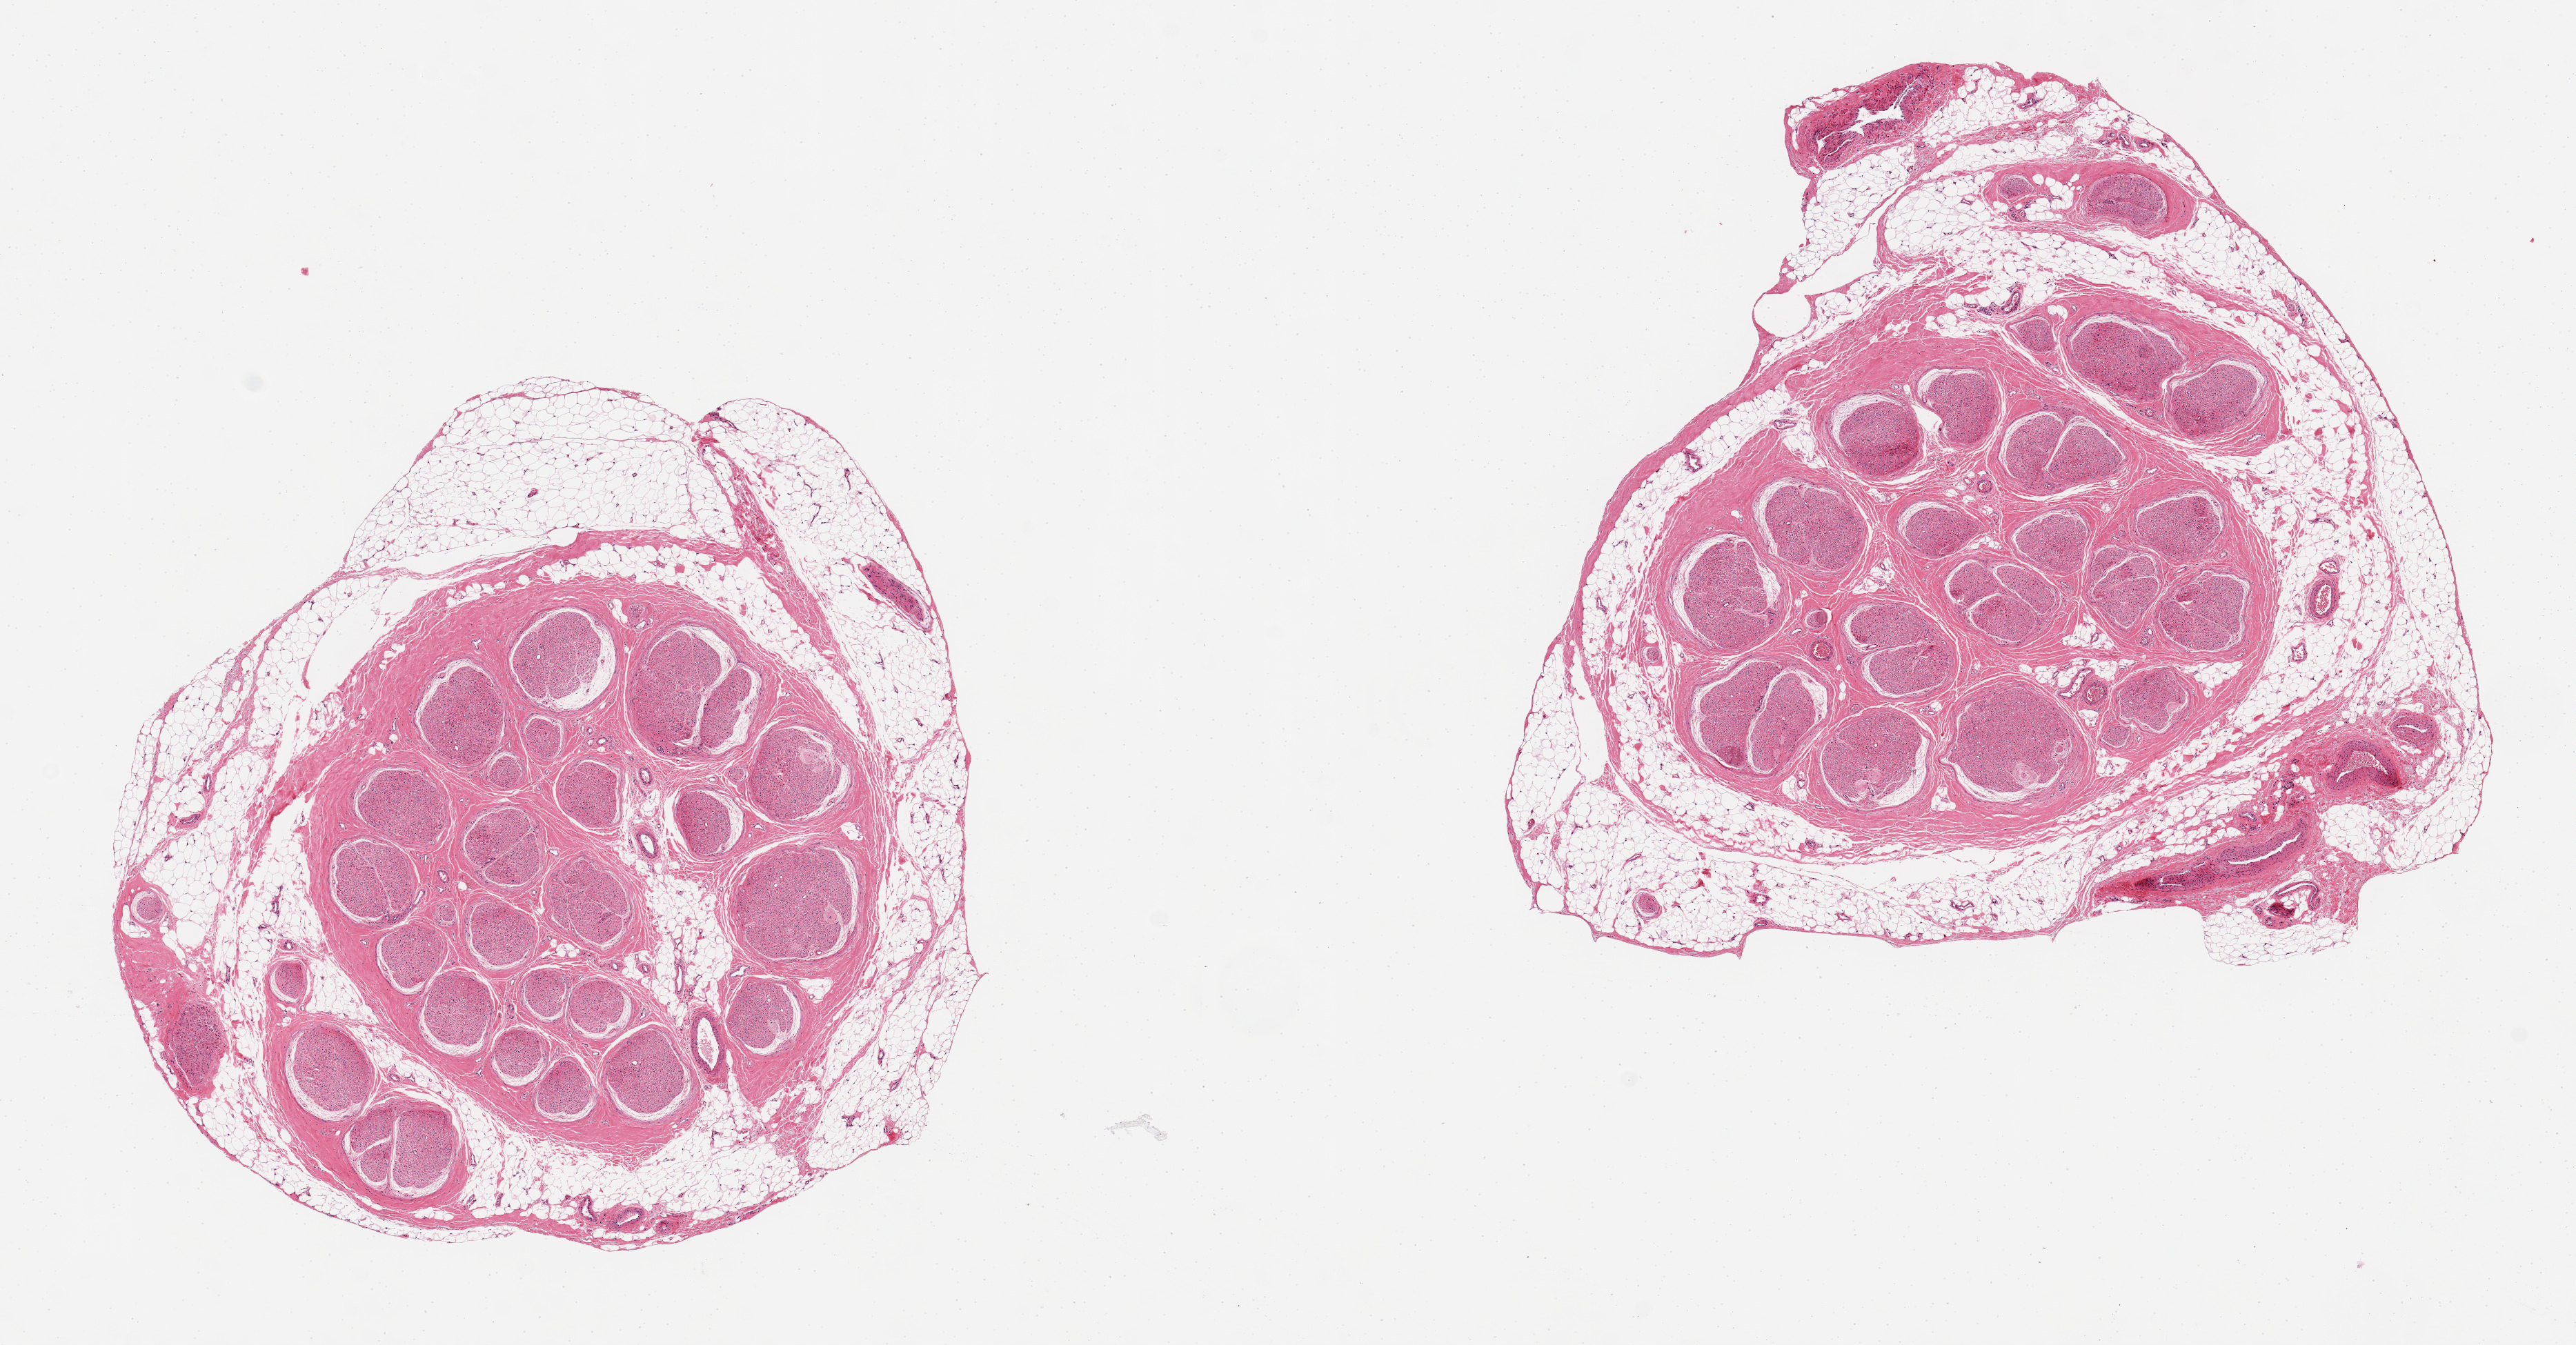
Digitized H&E-stained section, a low-resolution overview of the entire scanned area, about 14.8 x 7.7 mm. Donor sex: male.
* specimen: PAXgene-fixed paraffin-embedded (PFPE) section; target tissue: tibial nerve; donor tissue sample